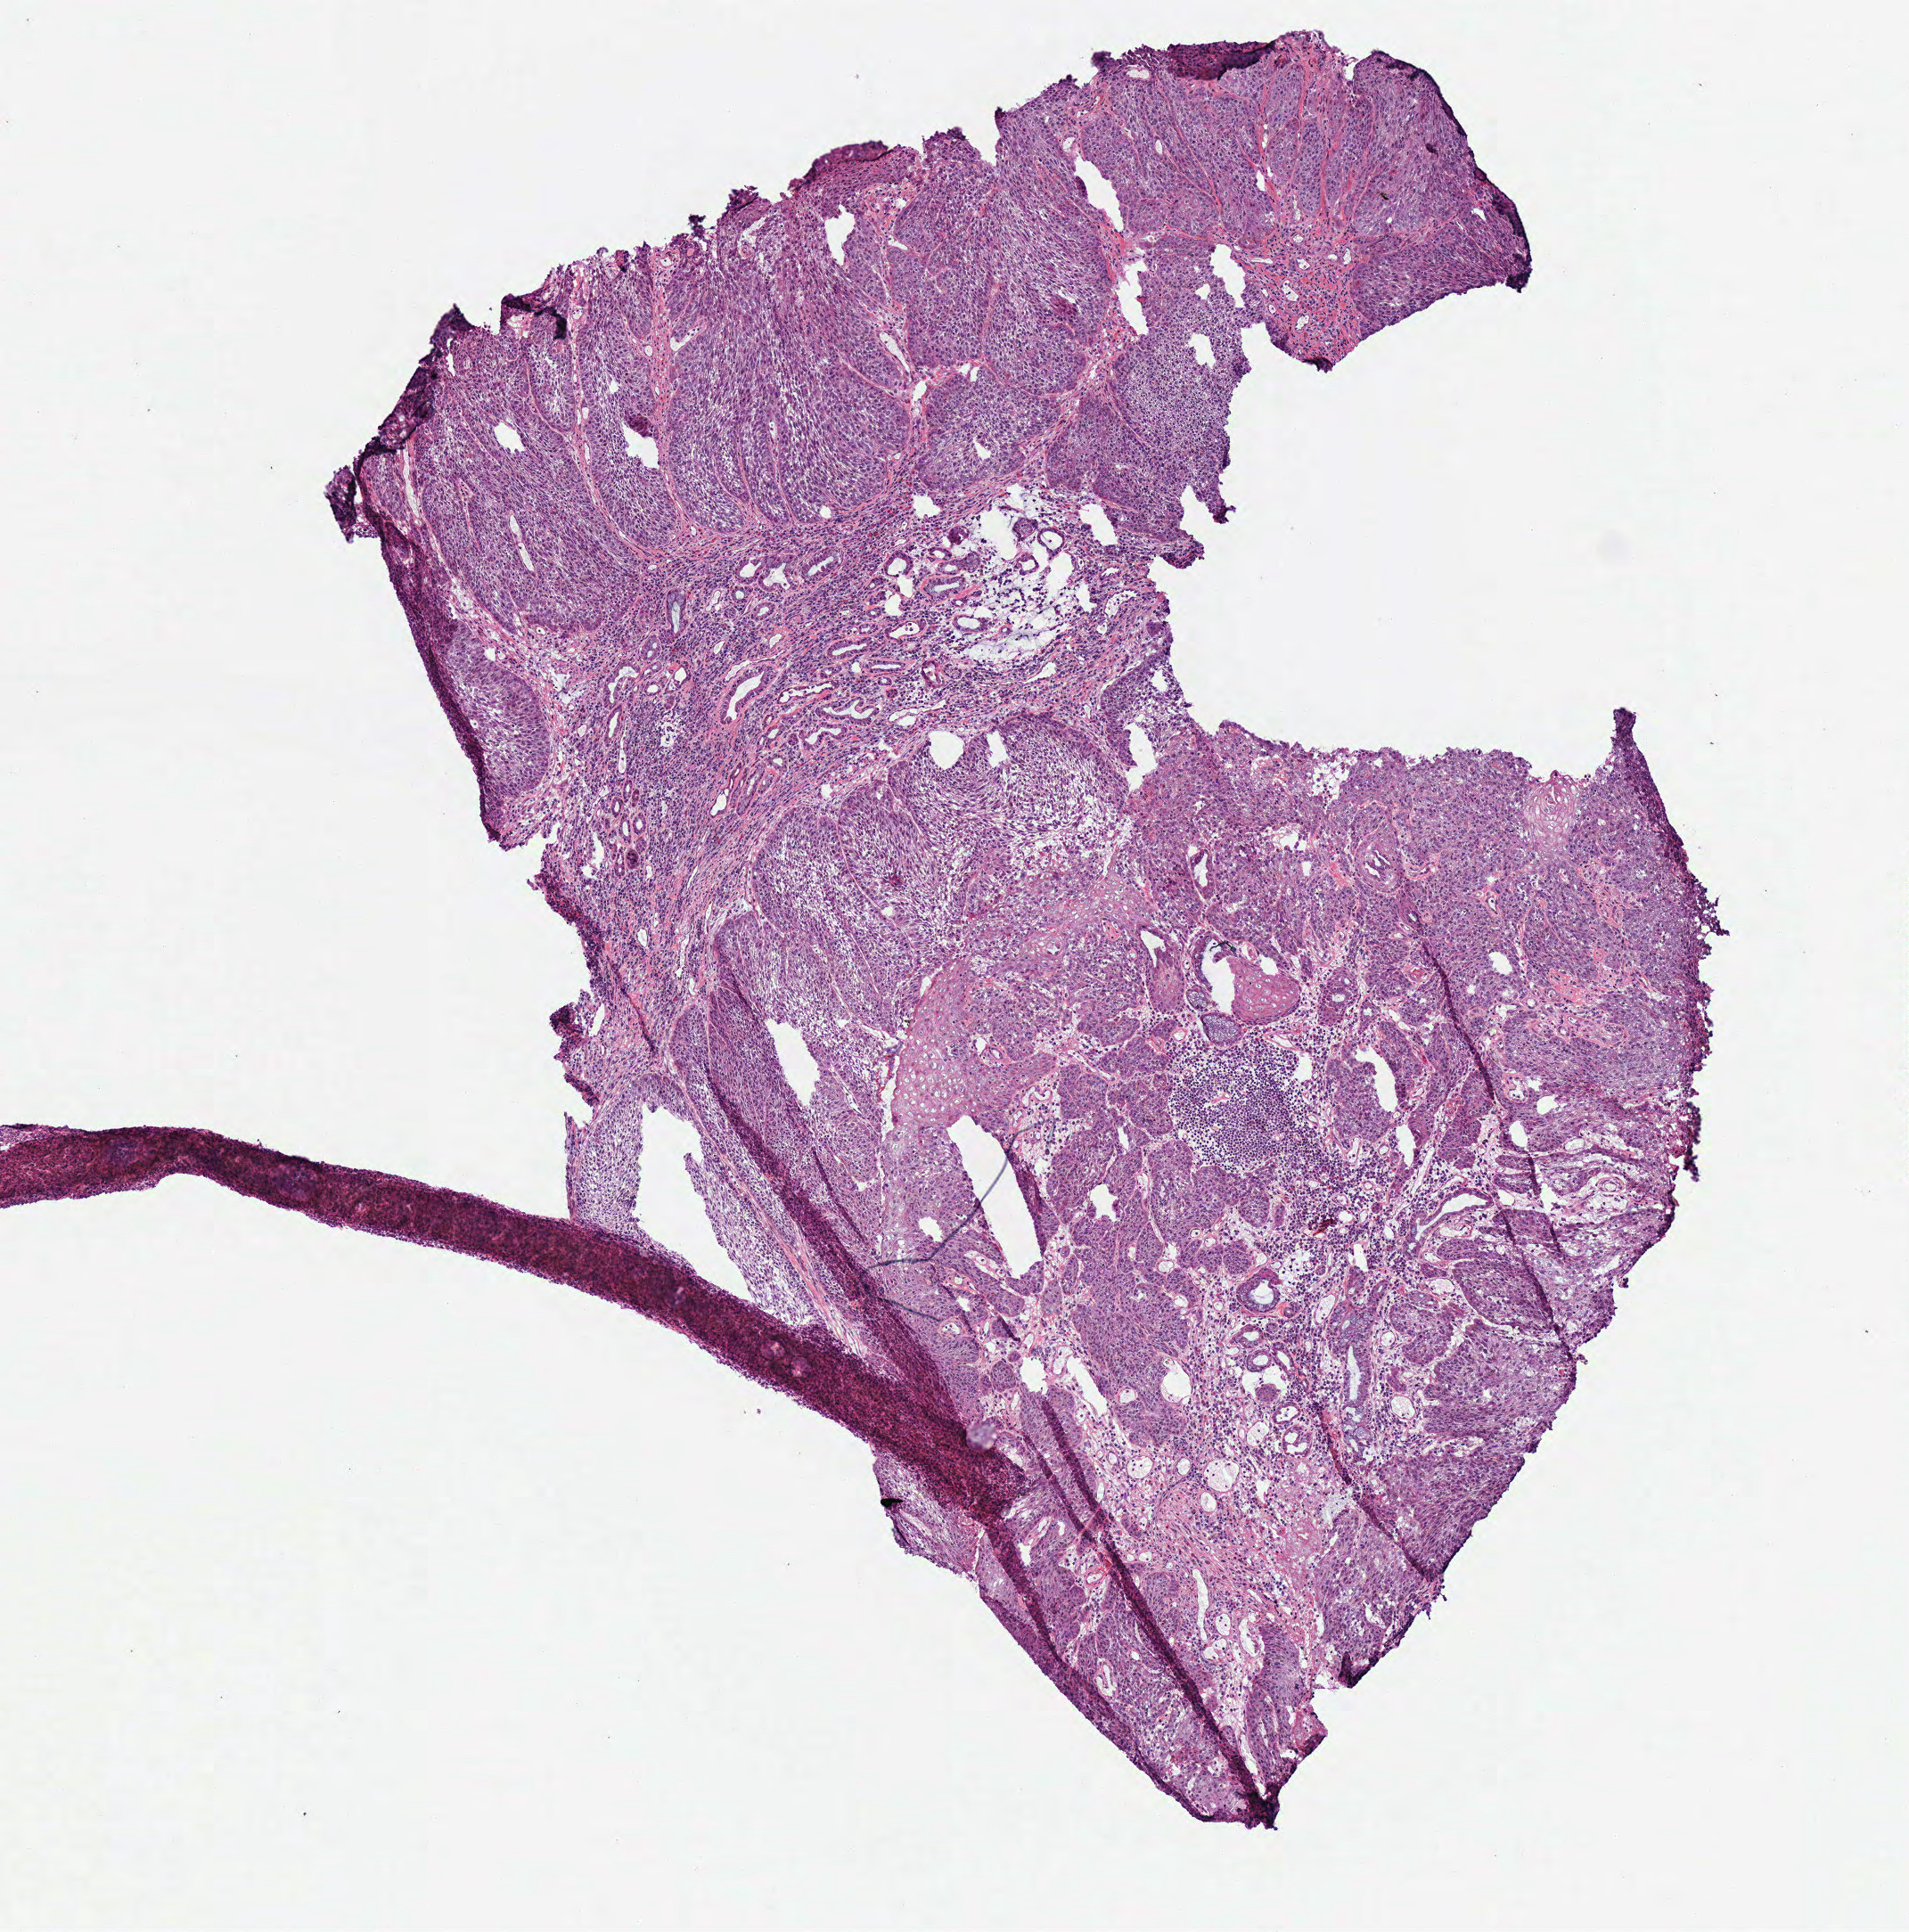
Digitized H&E tissue section (whole slide) — low-resolution overview of the scanned area, about 4.2 x 4.3 mm (slide scanned at 40x); frozen section from the top of the tissue portion; sample: primary tumour, head and neck. Male, age 62 years at initial diagnosis. Histologic grade: G2 (moderately differentiated). Composition of this section per pathologist review: tumour cells 85%, tumour nuclei 90%, normal cells 0%, stromal cells 14%, necrosis 1%. Inflammatory infiltration, as recorded: lymphocyte infiltration 2%.
* AJCC pathologic stage: III
* laterality: left
* histologic diagnosis: Squamous cell carcinoma, NOS (larynx, NOS)